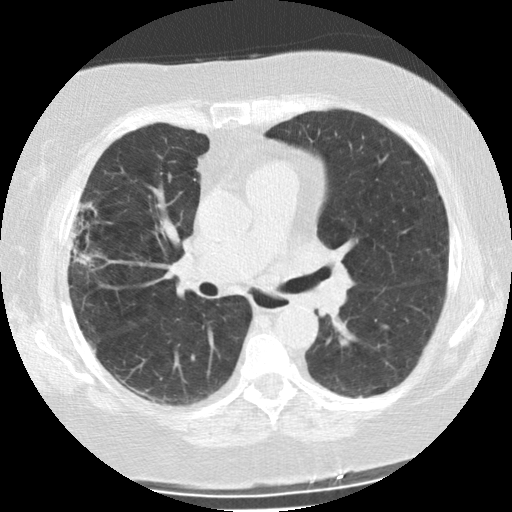
Low-dose screening chest CT, one axial slice. Slice 132 of 225 in the series (ordered by position). Reconstruction kernel STANDARD. 120 kVp. Lung window (W 1500 / L -600 HU). 512 × 512 image matrix, field of view 320 × 320 mm.
Outlined on this slice (expert manual segmentation):
- lesion 1 (tumor, upper lobe of right lung): bounding box [x1, y1, x2, y2] px = [72, 248, 99, 265]